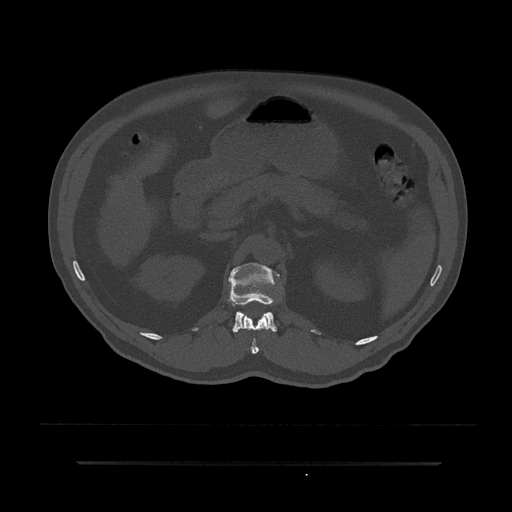
CT including the spine, one axial slice. Slice 176 of 797 in the series (ordered by position). Reconstruction kernel Br40s/3. 120 kVp. Bone window (W 1800 / L 400 HU). 512 × 512 image matrix. Patient: male, 59 years. From the clinical record (not read from this slice): primary cancer: bile ducts; vertebrae with lytic lesions (as recorded): T10.
Structures marked on this image (semi-automatically segmented with operator editing):
- L1 vertebra: bounding box [x1, y1, x2, y2] px = [229, 263, 279, 333]
- T12 vertebra: [241, 315, 269, 354]